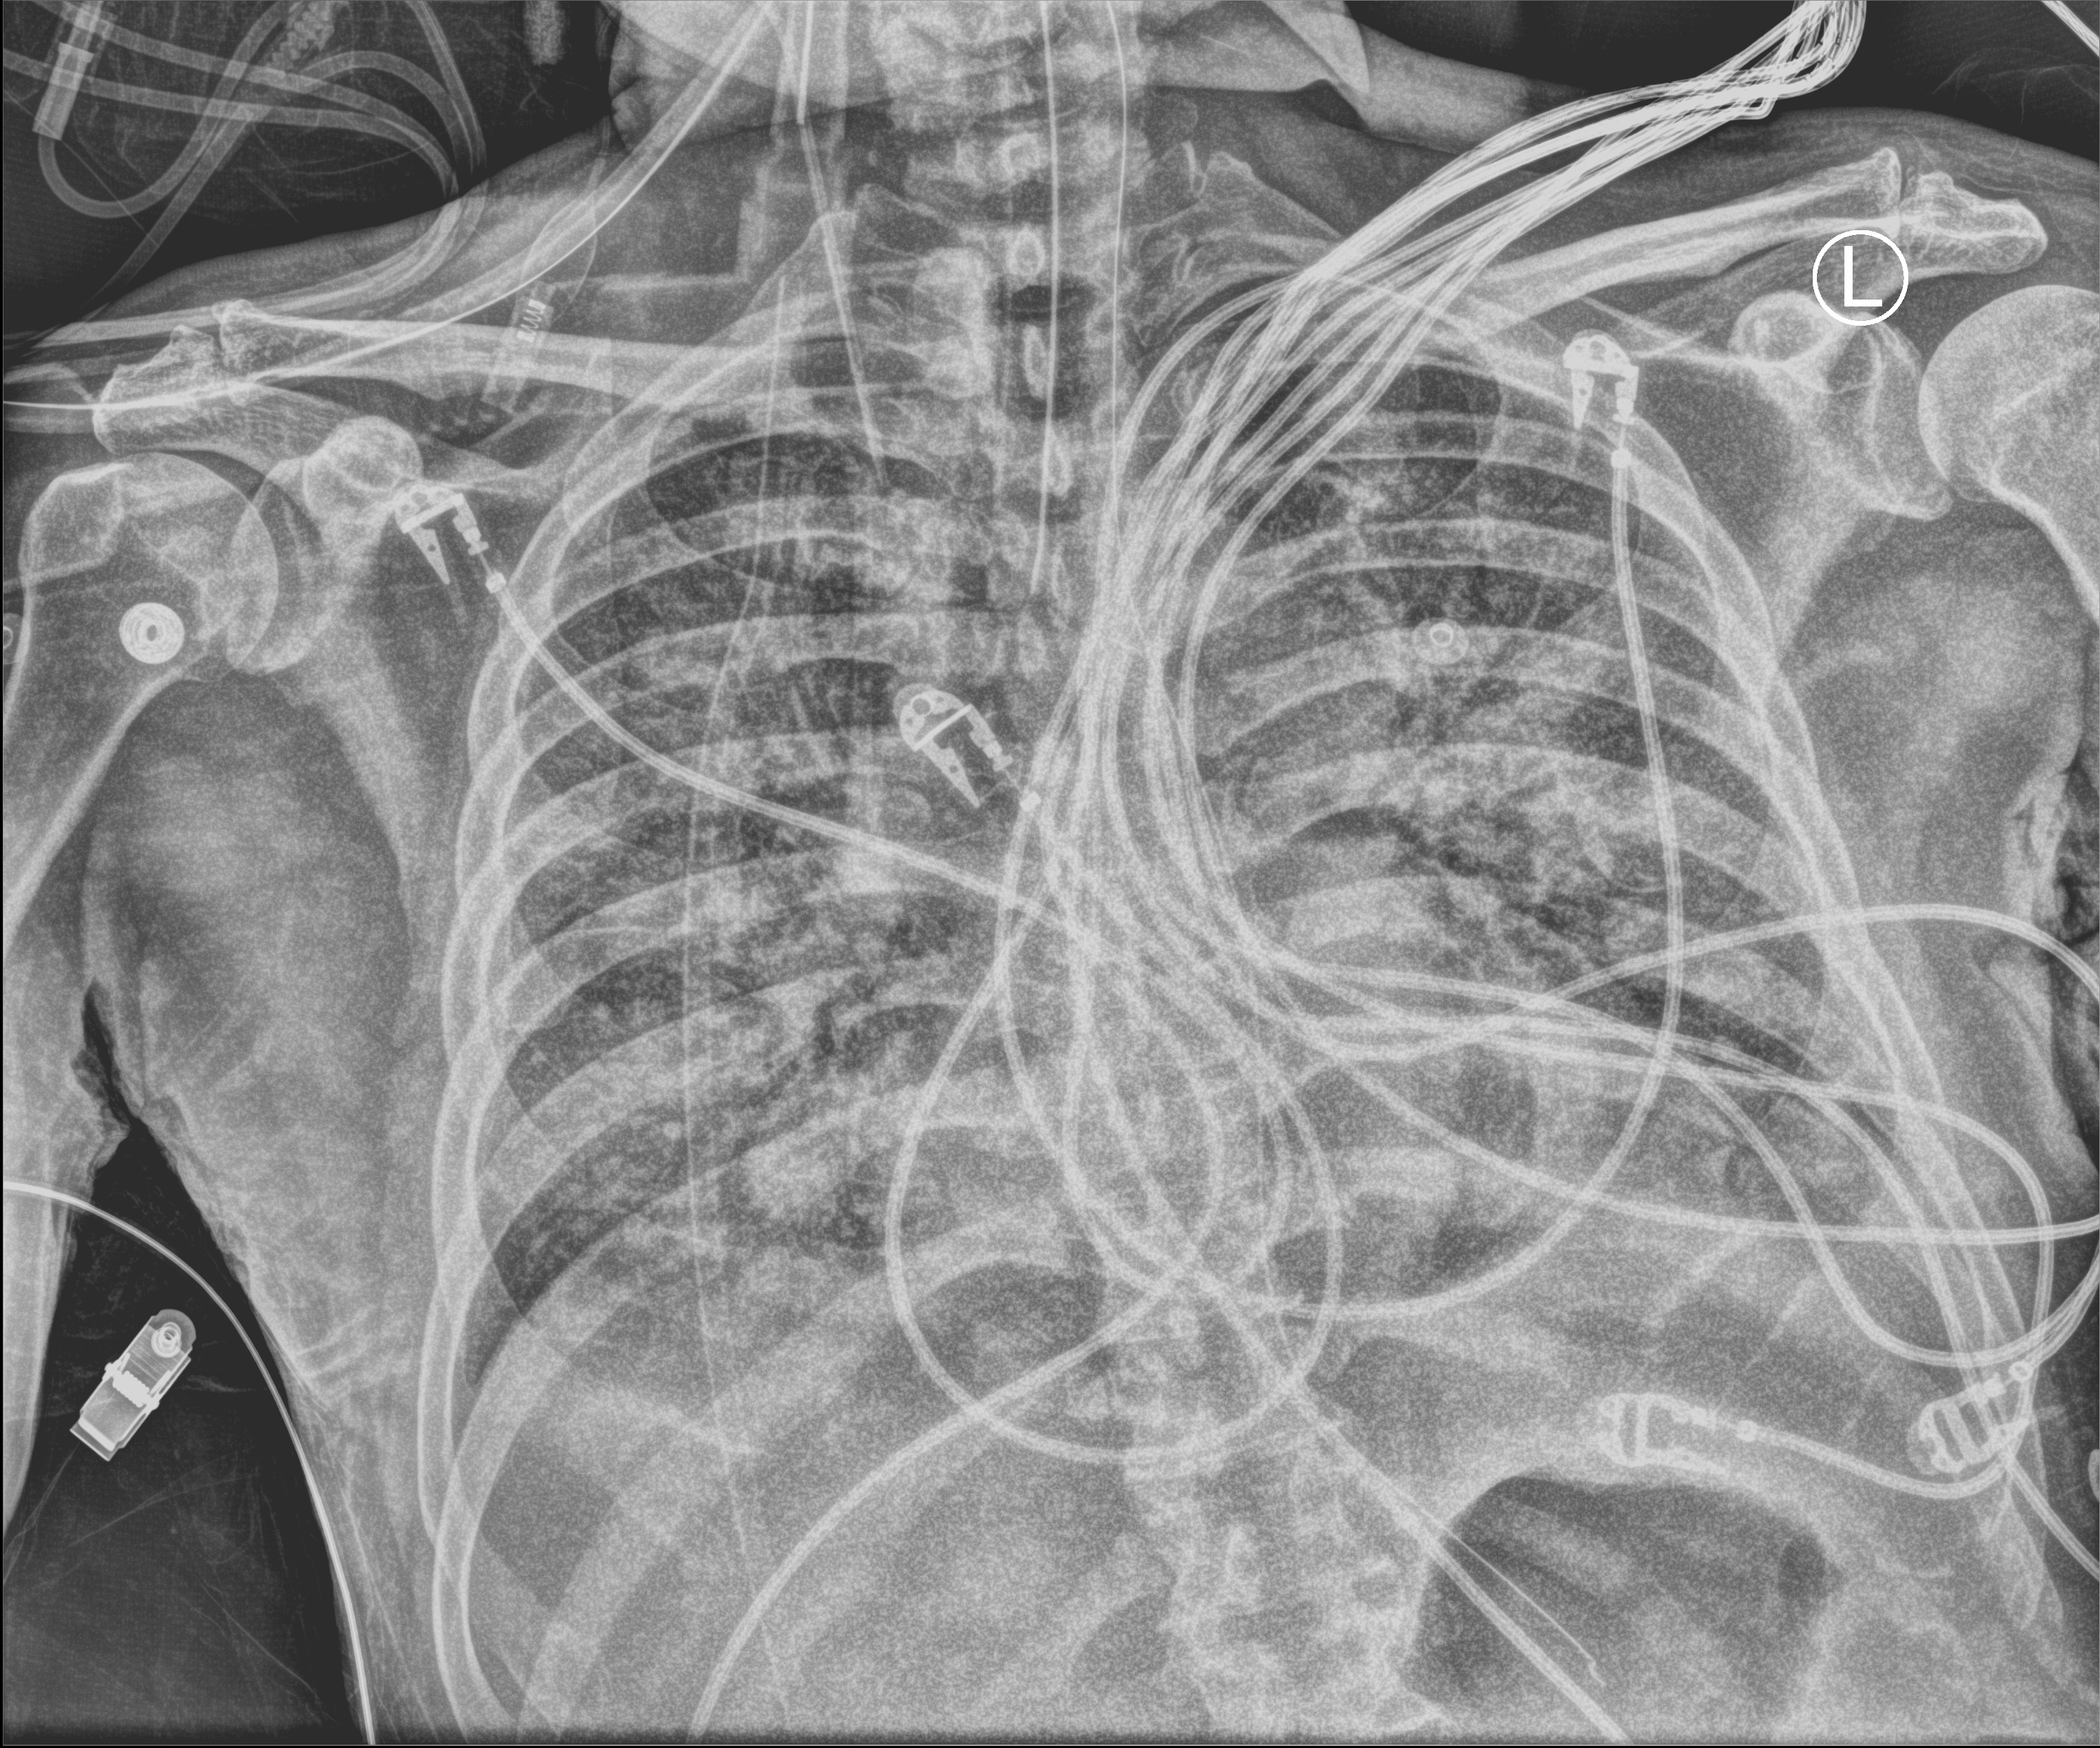
Bedside chest radiograph (computed radiography); anteroposterior (AP) projection. Male patient hospitalised with COVID-19, age 60–74 years.
From the hospital-stay record, not from the radiograph (when in the stay this image was taken is not recorded):
- diabetes (admission record): no